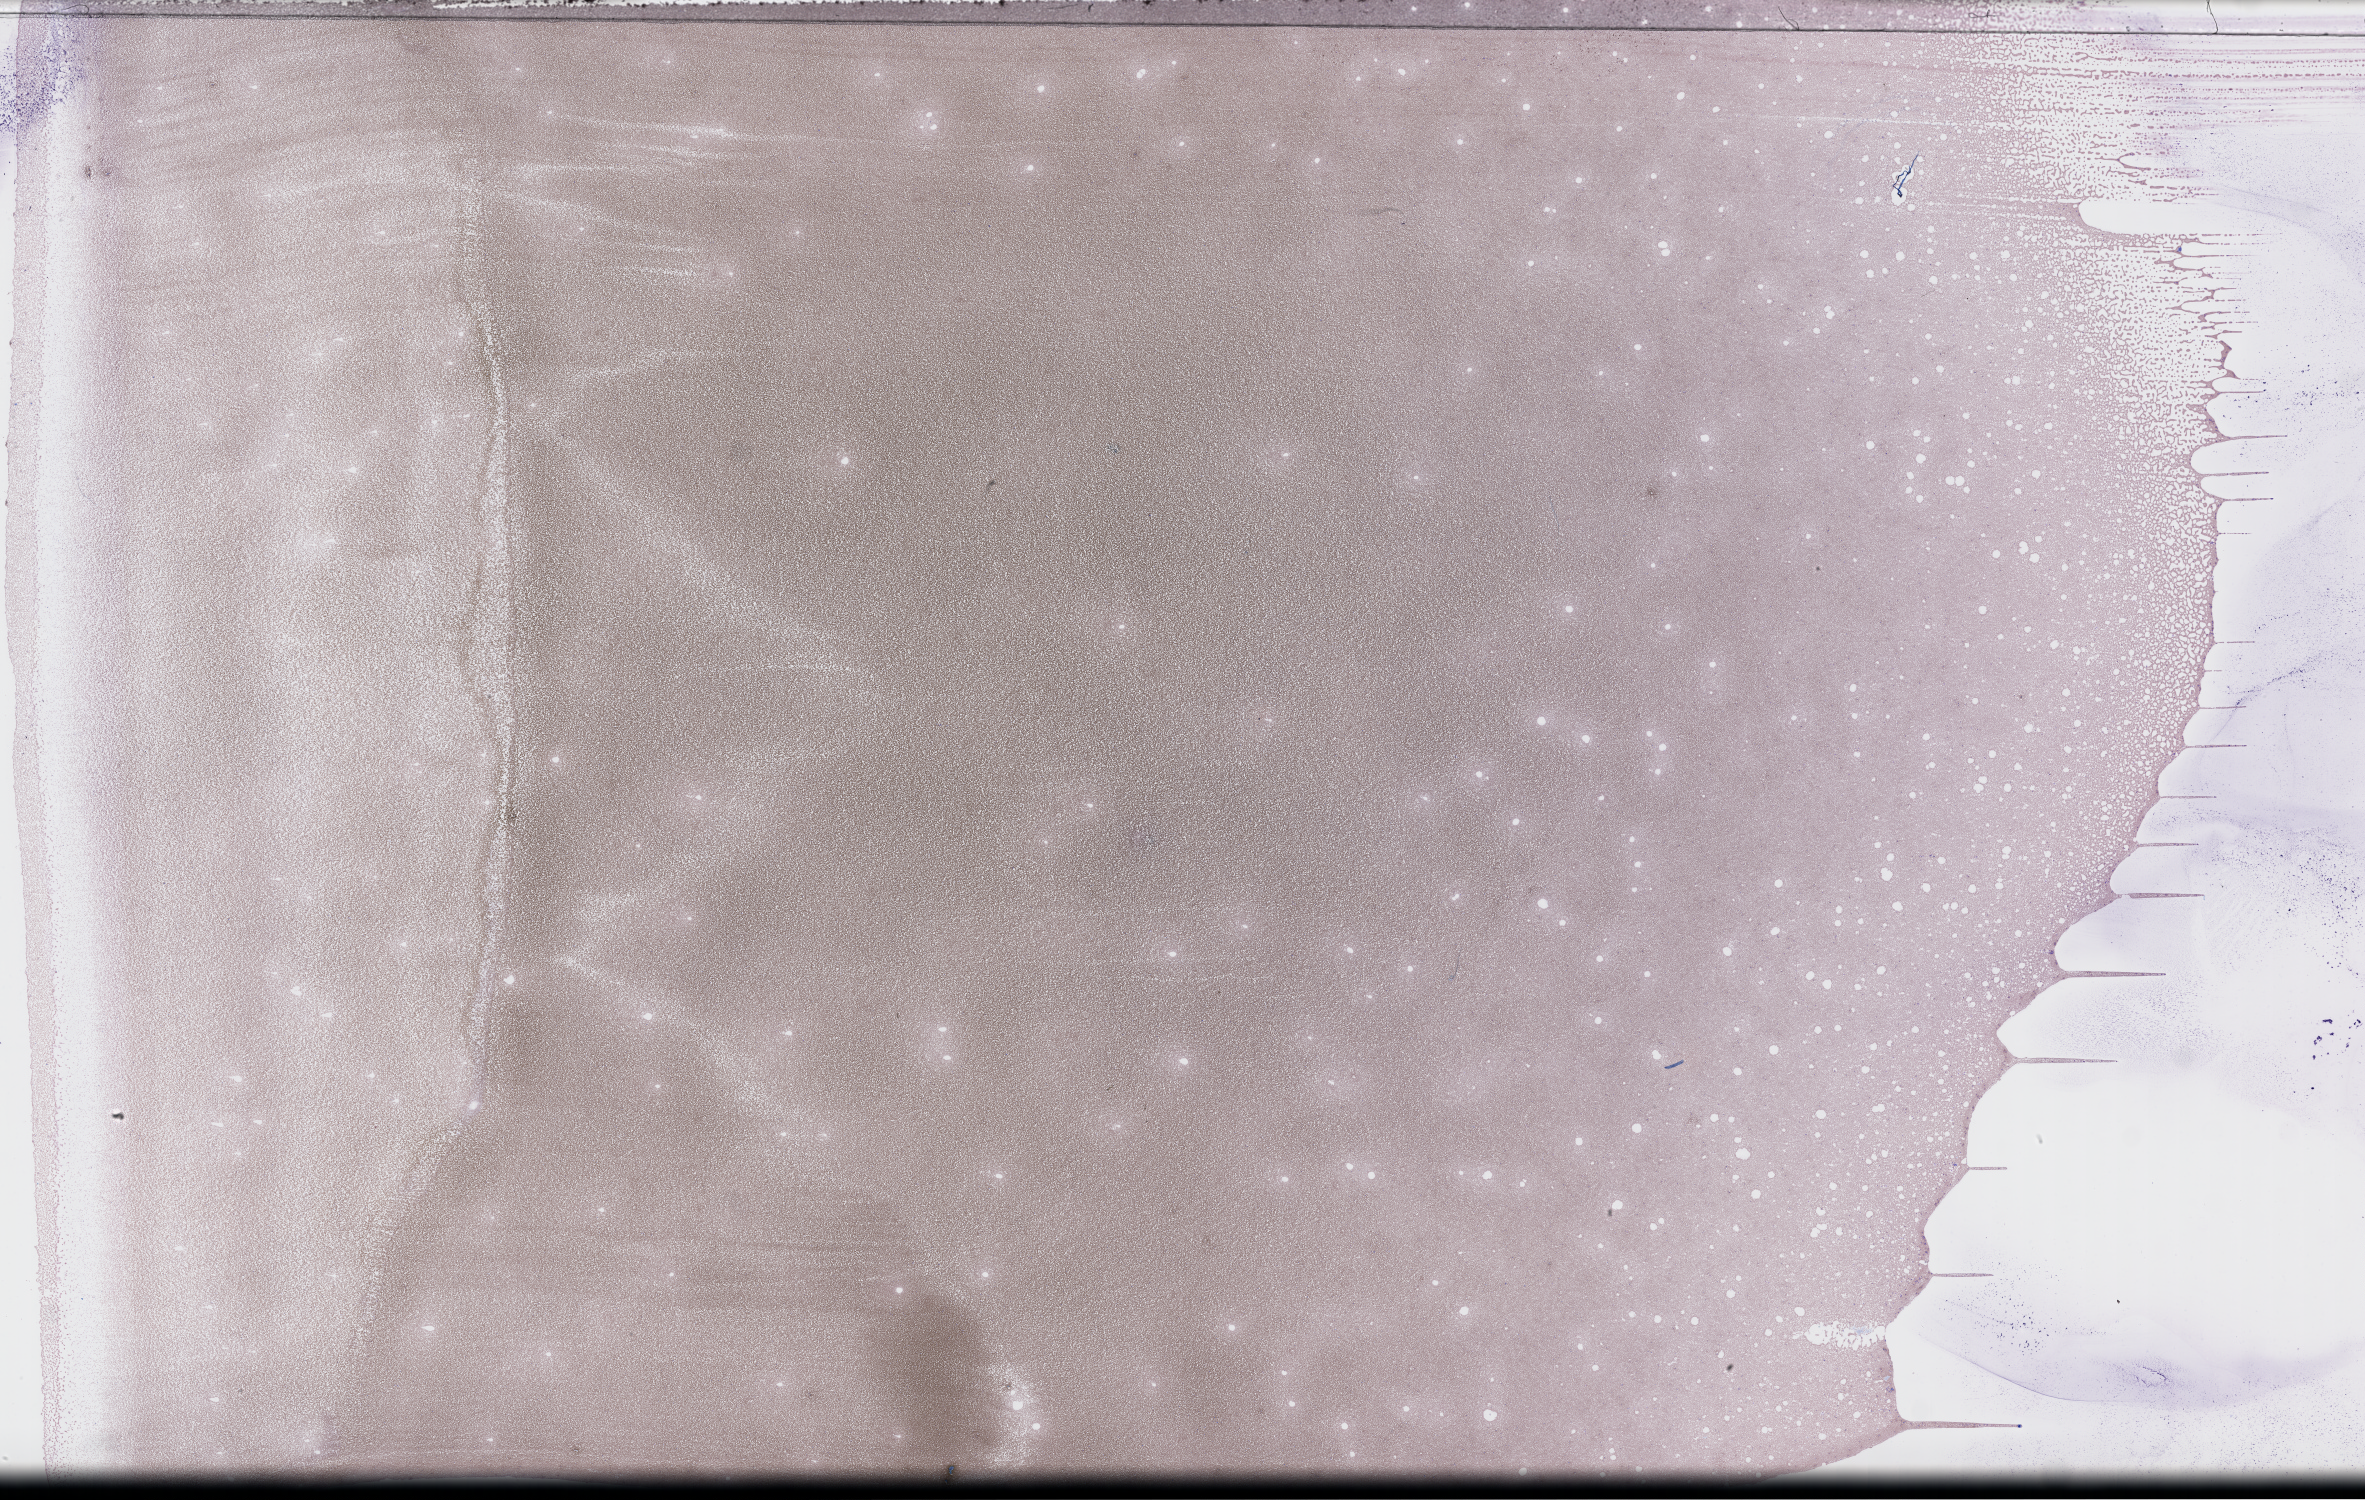
Whole-slide image of a whole blood smear, Wright–Giemsa stain — a low-resolution overview of the entire scanned area, about 38.2 x 24.2 mm, specimen time point: collected on treatment. Female patient.
- patient diagnosis: Plasma Cell Myeloma